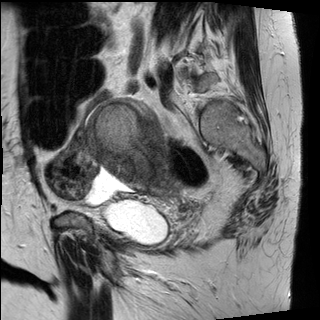
Pelvic MRI for cervical cancer, one sagittal slice. Slice 21 of 30 in the series (ordered by position). T2-weighted. 1.5 T. TE 89 ms, TR 2930 ms. 320 × 320 image matrix, field of view 260 × 260 mm. Patient: female, 62 years.
Structures marked on this image (outlined manually by an expert reader):
- uterus and cervix: bounding box (x1, y1, x2, y2) in pixels: (87, 97, 184, 196)